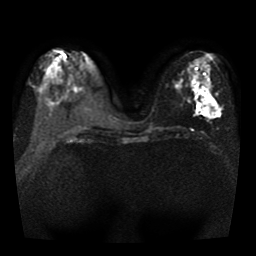
Breast MRI, one axial slice. Position 16 of 41 along the scan axis. Diffusion-weighted series; image 2 of 4 stored at this slice position (different b-values; order by instance number). 1.5 T. 5 mm slice thickness. 256 × 256 image matrix, field of view 330 × 330 mm. Female patient.
Annotated regions visible in this slice (expert manual segmentation):
- tumour on diffusion-weighted imaging: bounding box [x1, y1, x2, y2] px = [204, 99, 220, 116]